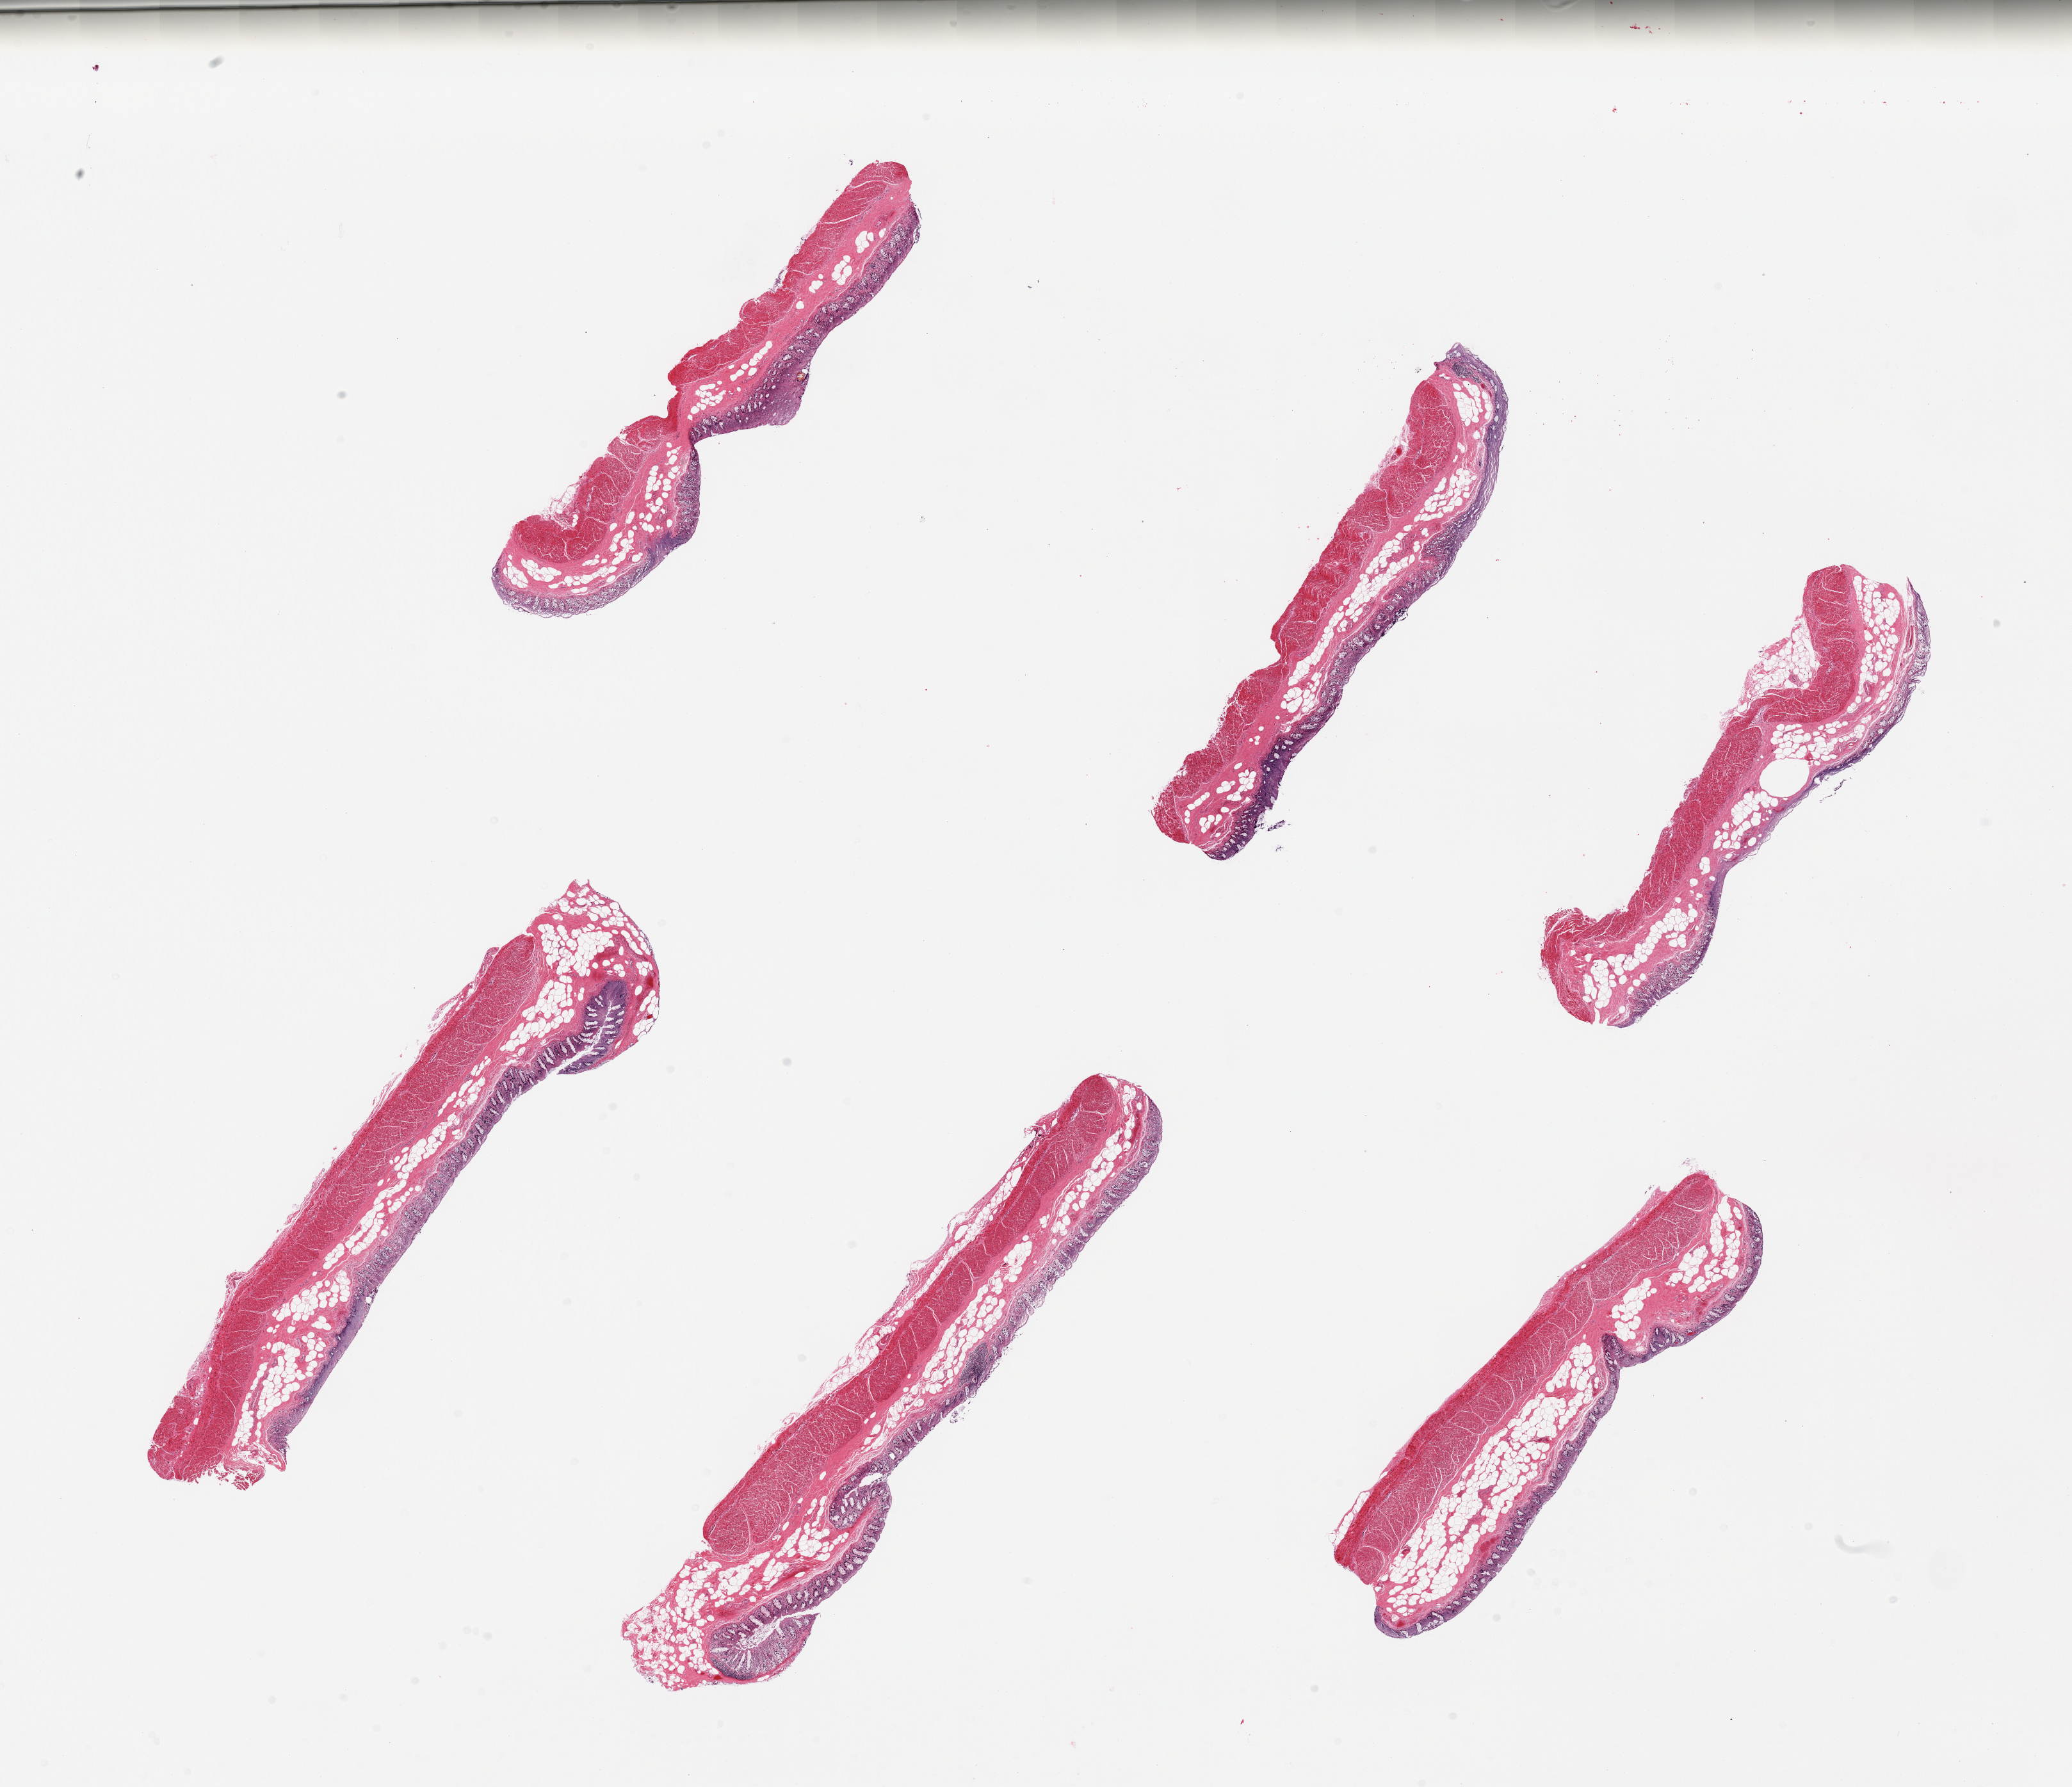
Whole-slide image, hematoxylin and eosin (H&E) stain — a low-resolution overview of the entire scanned area, about 25.6 x 22.1 mm; PAXgene-fixed, paraffin-embedded tissue; sampled site (target tissue): transverse colon; tissue donor sample. Male donor.
* reviewer comment on this tissue sample: 6 pieces